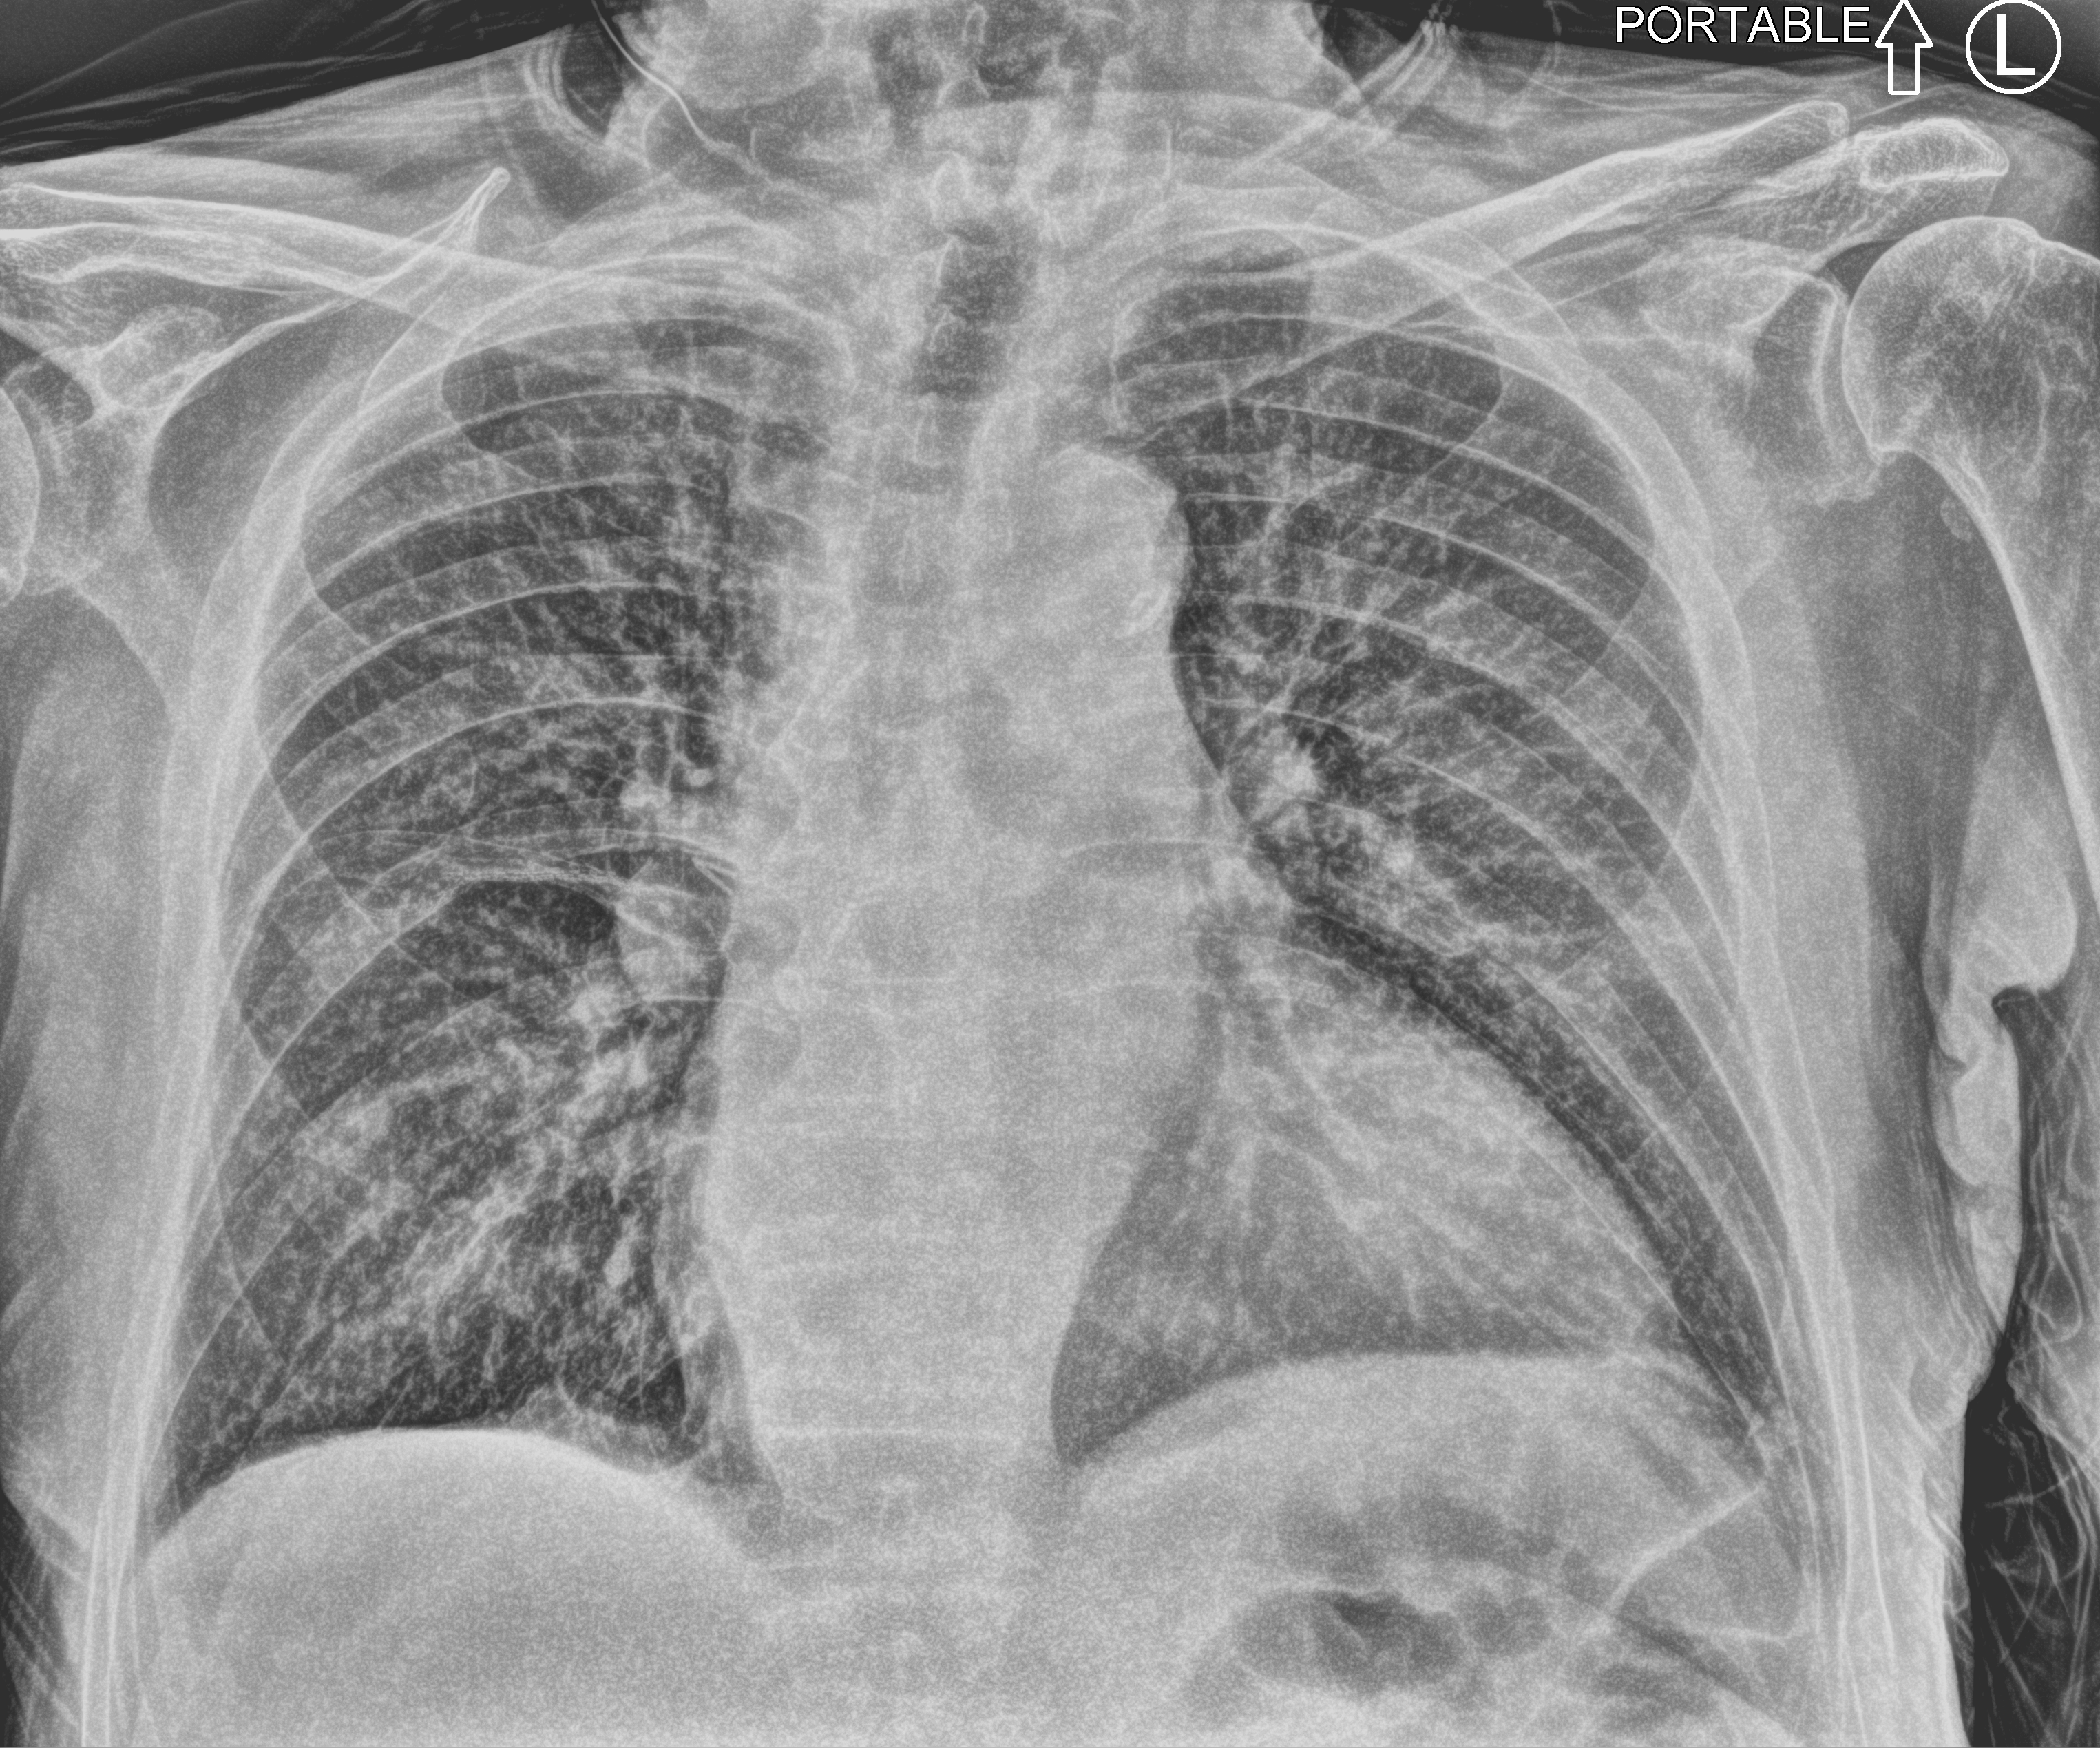
Bedside chest radiograph (computed radiography); anteroposterior (AP) projection. Male patient hospitalised with COVID-19, age 75–90 years.
From the hospital-stay record, not from the radiograph (when in the stay this image was taken is not recorded):
- mechanically ventilated during this hospital stay: no
- COPD (admission record): no